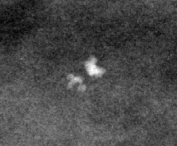
Crop from a digitized film mammogram around one marked abnormality; right breast; CC view; BI-RADS breast density category 4 (scale 1–4).
Marked abnormality: calcifications, morphology round and regular / lucent center / punctate, distribution diffusely scattered; BI-RADS assessment category 2; benign; no additional work-up was recommended (benign without callback).